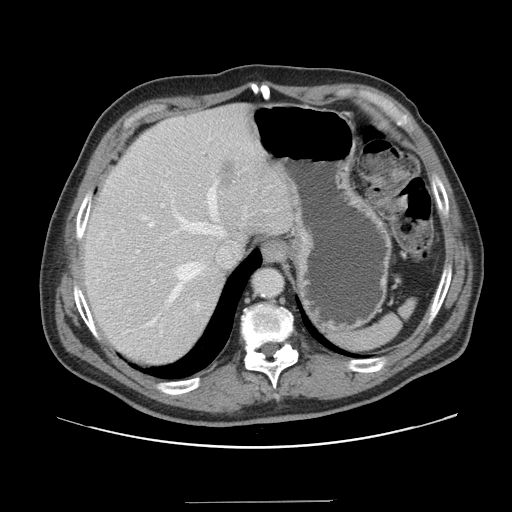
Contrast-enhanced abdominal CT, one axial slice. Slice 123 of 151 in the series (ordered by position). 120 kVp. Soft-tissue window (W 400 / L 40 HU). 2.5 mm slice thickness. 512 × 512 image matrix. Male patient, age 63 years. Case-level facts recorded for this patient, not image findings: diagnosis: colorectal cancer liver metastases, imaged before liver resection; multiple liver metastases: no; largest metastasis: 2.1 cm; disease in both lobes: no.
Structures marked on this image (expert manual segmentation):
- hepatic veins: bounding box (x1, y1, x2, y2) in pixels: (142, 184, 224, 325)
- liver: (83, 106, 294, 366)
- planned liver remnant (the part of the liver to remain after resection): (84, 118, 254, 366)
- portal vein (with intrahepatic branches): (136, 204, 164, 283)
- liver metastasis: (218, 161, 238, 190)